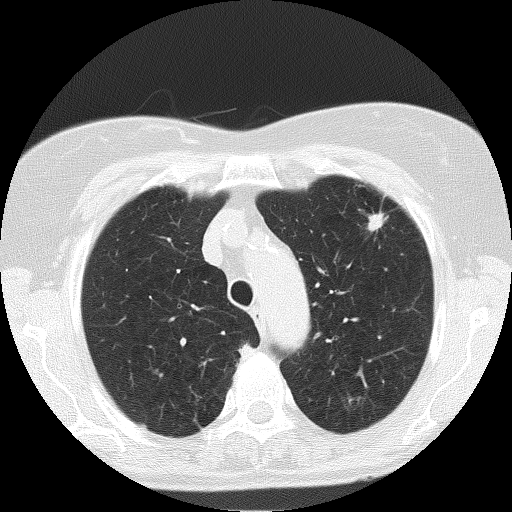
Low-dose screening chest CT, one axial slice; position 133 of 166 along the scan axis; reconstruction kernel FC51; 120 kVp; lung window (W 1500 / L -600 HU); 2 mm slice thickness; 512 × 512 image matrix, field of view 303 × 303 mm.
Outlined on this slice (expert manual segmentation):
- lesion 1 (tumor, upper lobe of left lung): bounding box <368,213,385,230> (left, top, right, bottom; pixels)